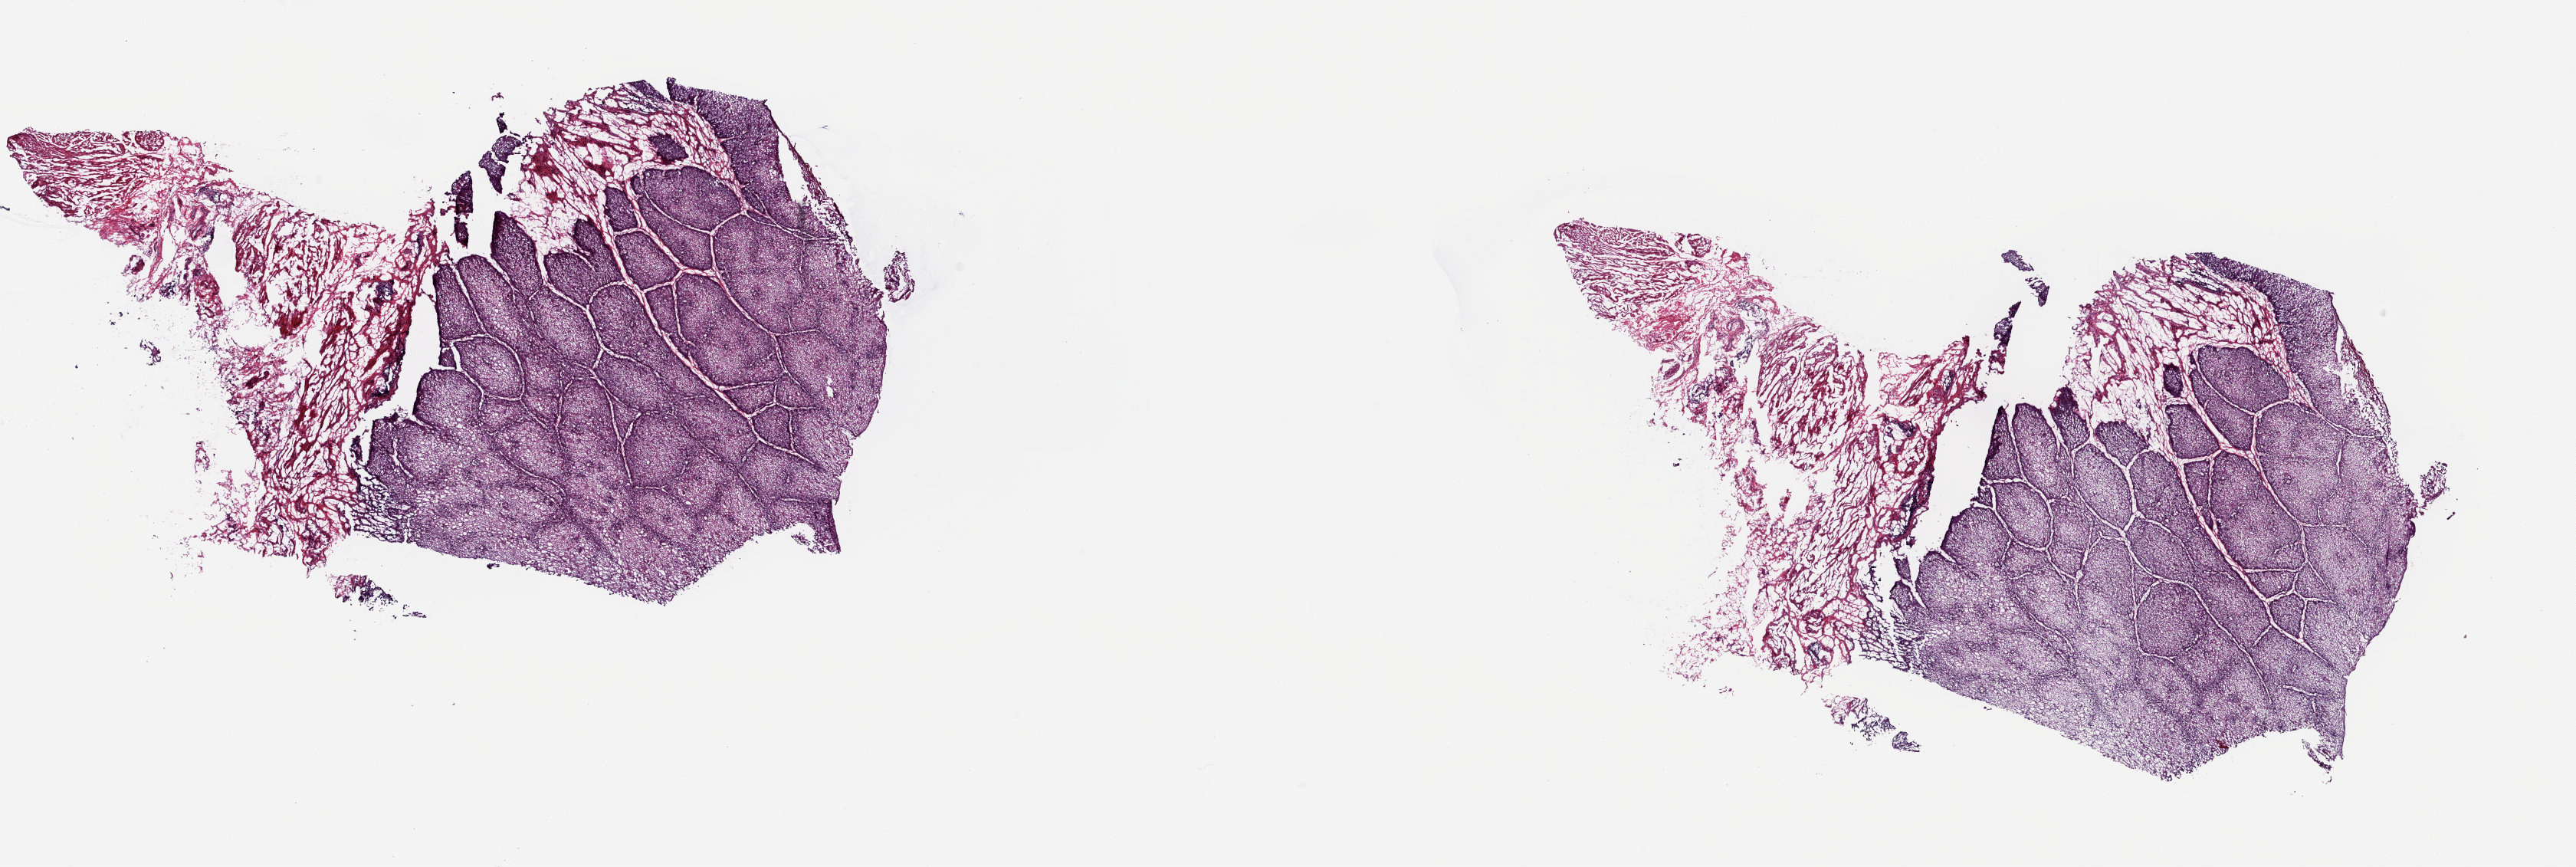
Whole-slide histology image, Hematoxylin and eosin (H&E) stained — shown as a low-resolution overview of the whole scanned area (about 26.7 x 9.0 mm, from a 20x scan). Frozen section. Bladder, solid tissue normal (non-tumour tissue) sample. Female, age 70 years at initial diagnosis. Composition of this section per pathologist review: tumour cells 0%, tumour nuclei 0%, normal cells 100%, stromal cells 0%, necrosis 0%. Inflammatory infiltration, as recorded: lymphocyte infiltration 0%, monocyte infiltration 0%, neutrophil infiltration 0%.
This section: solid tissue normal sample (biorepository sample class). Patient diagnosis: Transitional cell carcinoma (trigone of bladder).